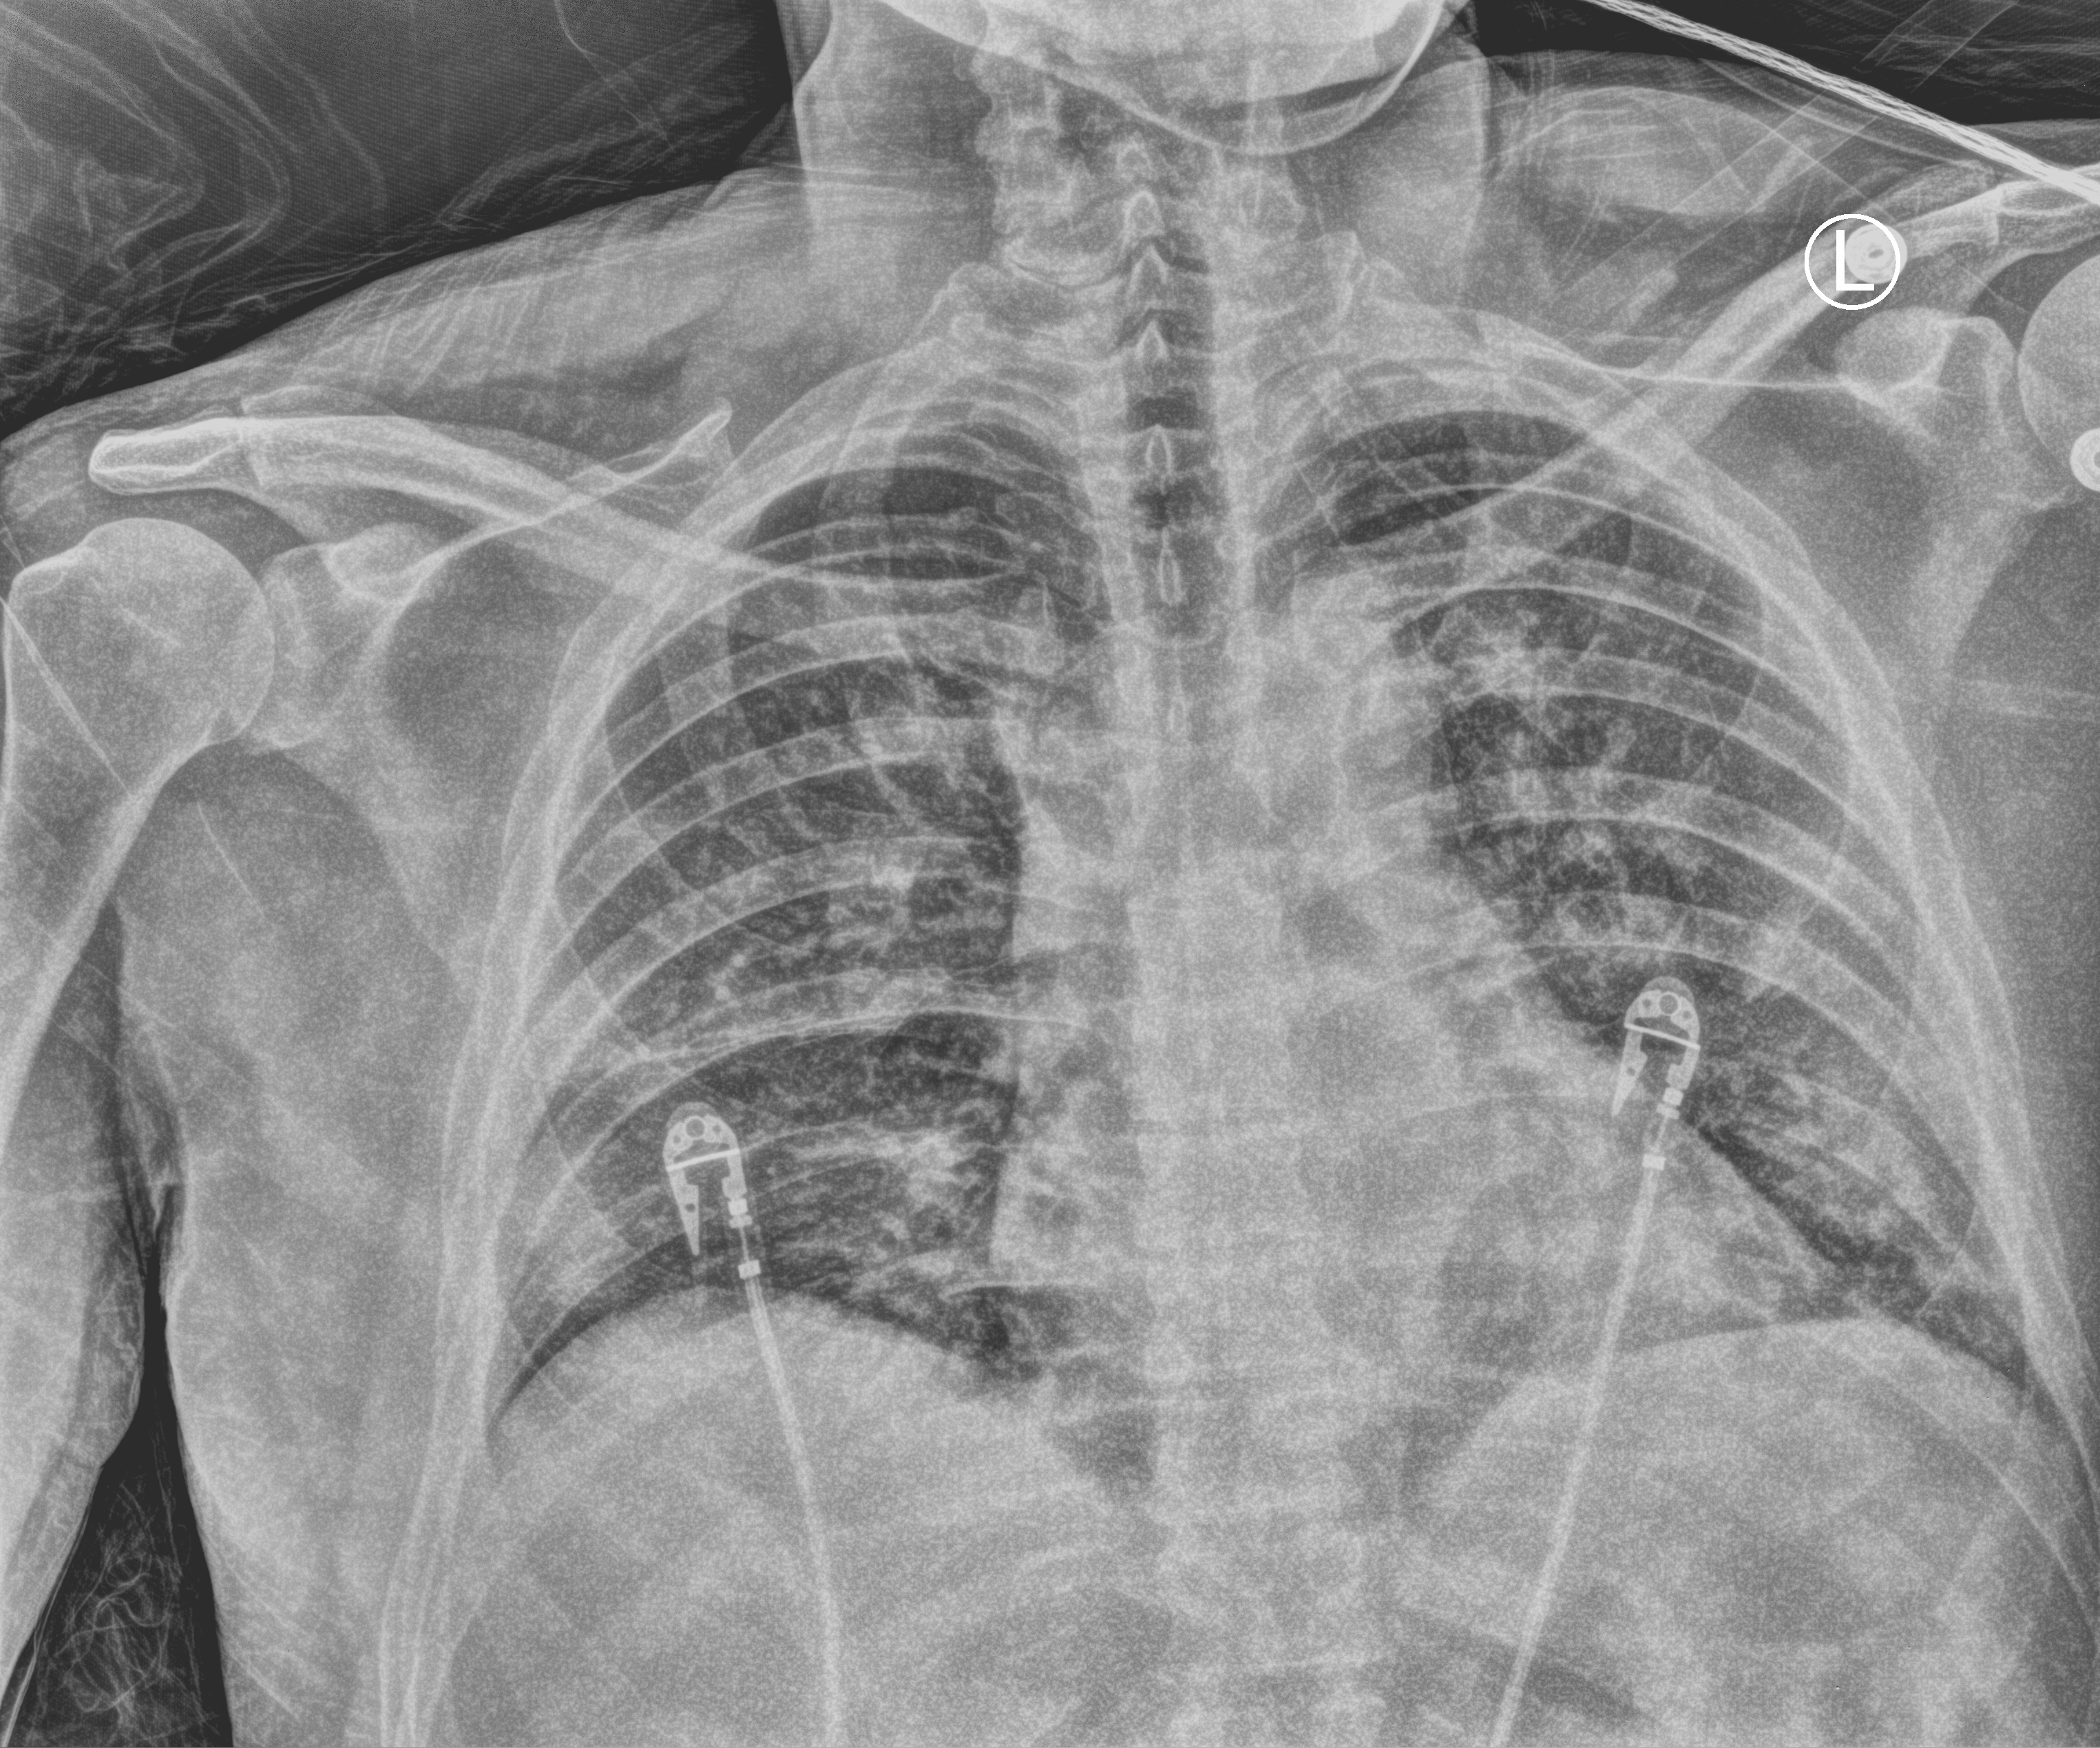
Chest X-ray (portable), anteroposterior (AP) projection. Male patient hospitalised with COVID-19, age 18–59 years.
Hospital-stay facts (about this admission, not read from this image; timing relative to this image not recorded):
- admitted to intensive care during this hospital stay: yes
- mechanically ventilated during this hospital stay: no